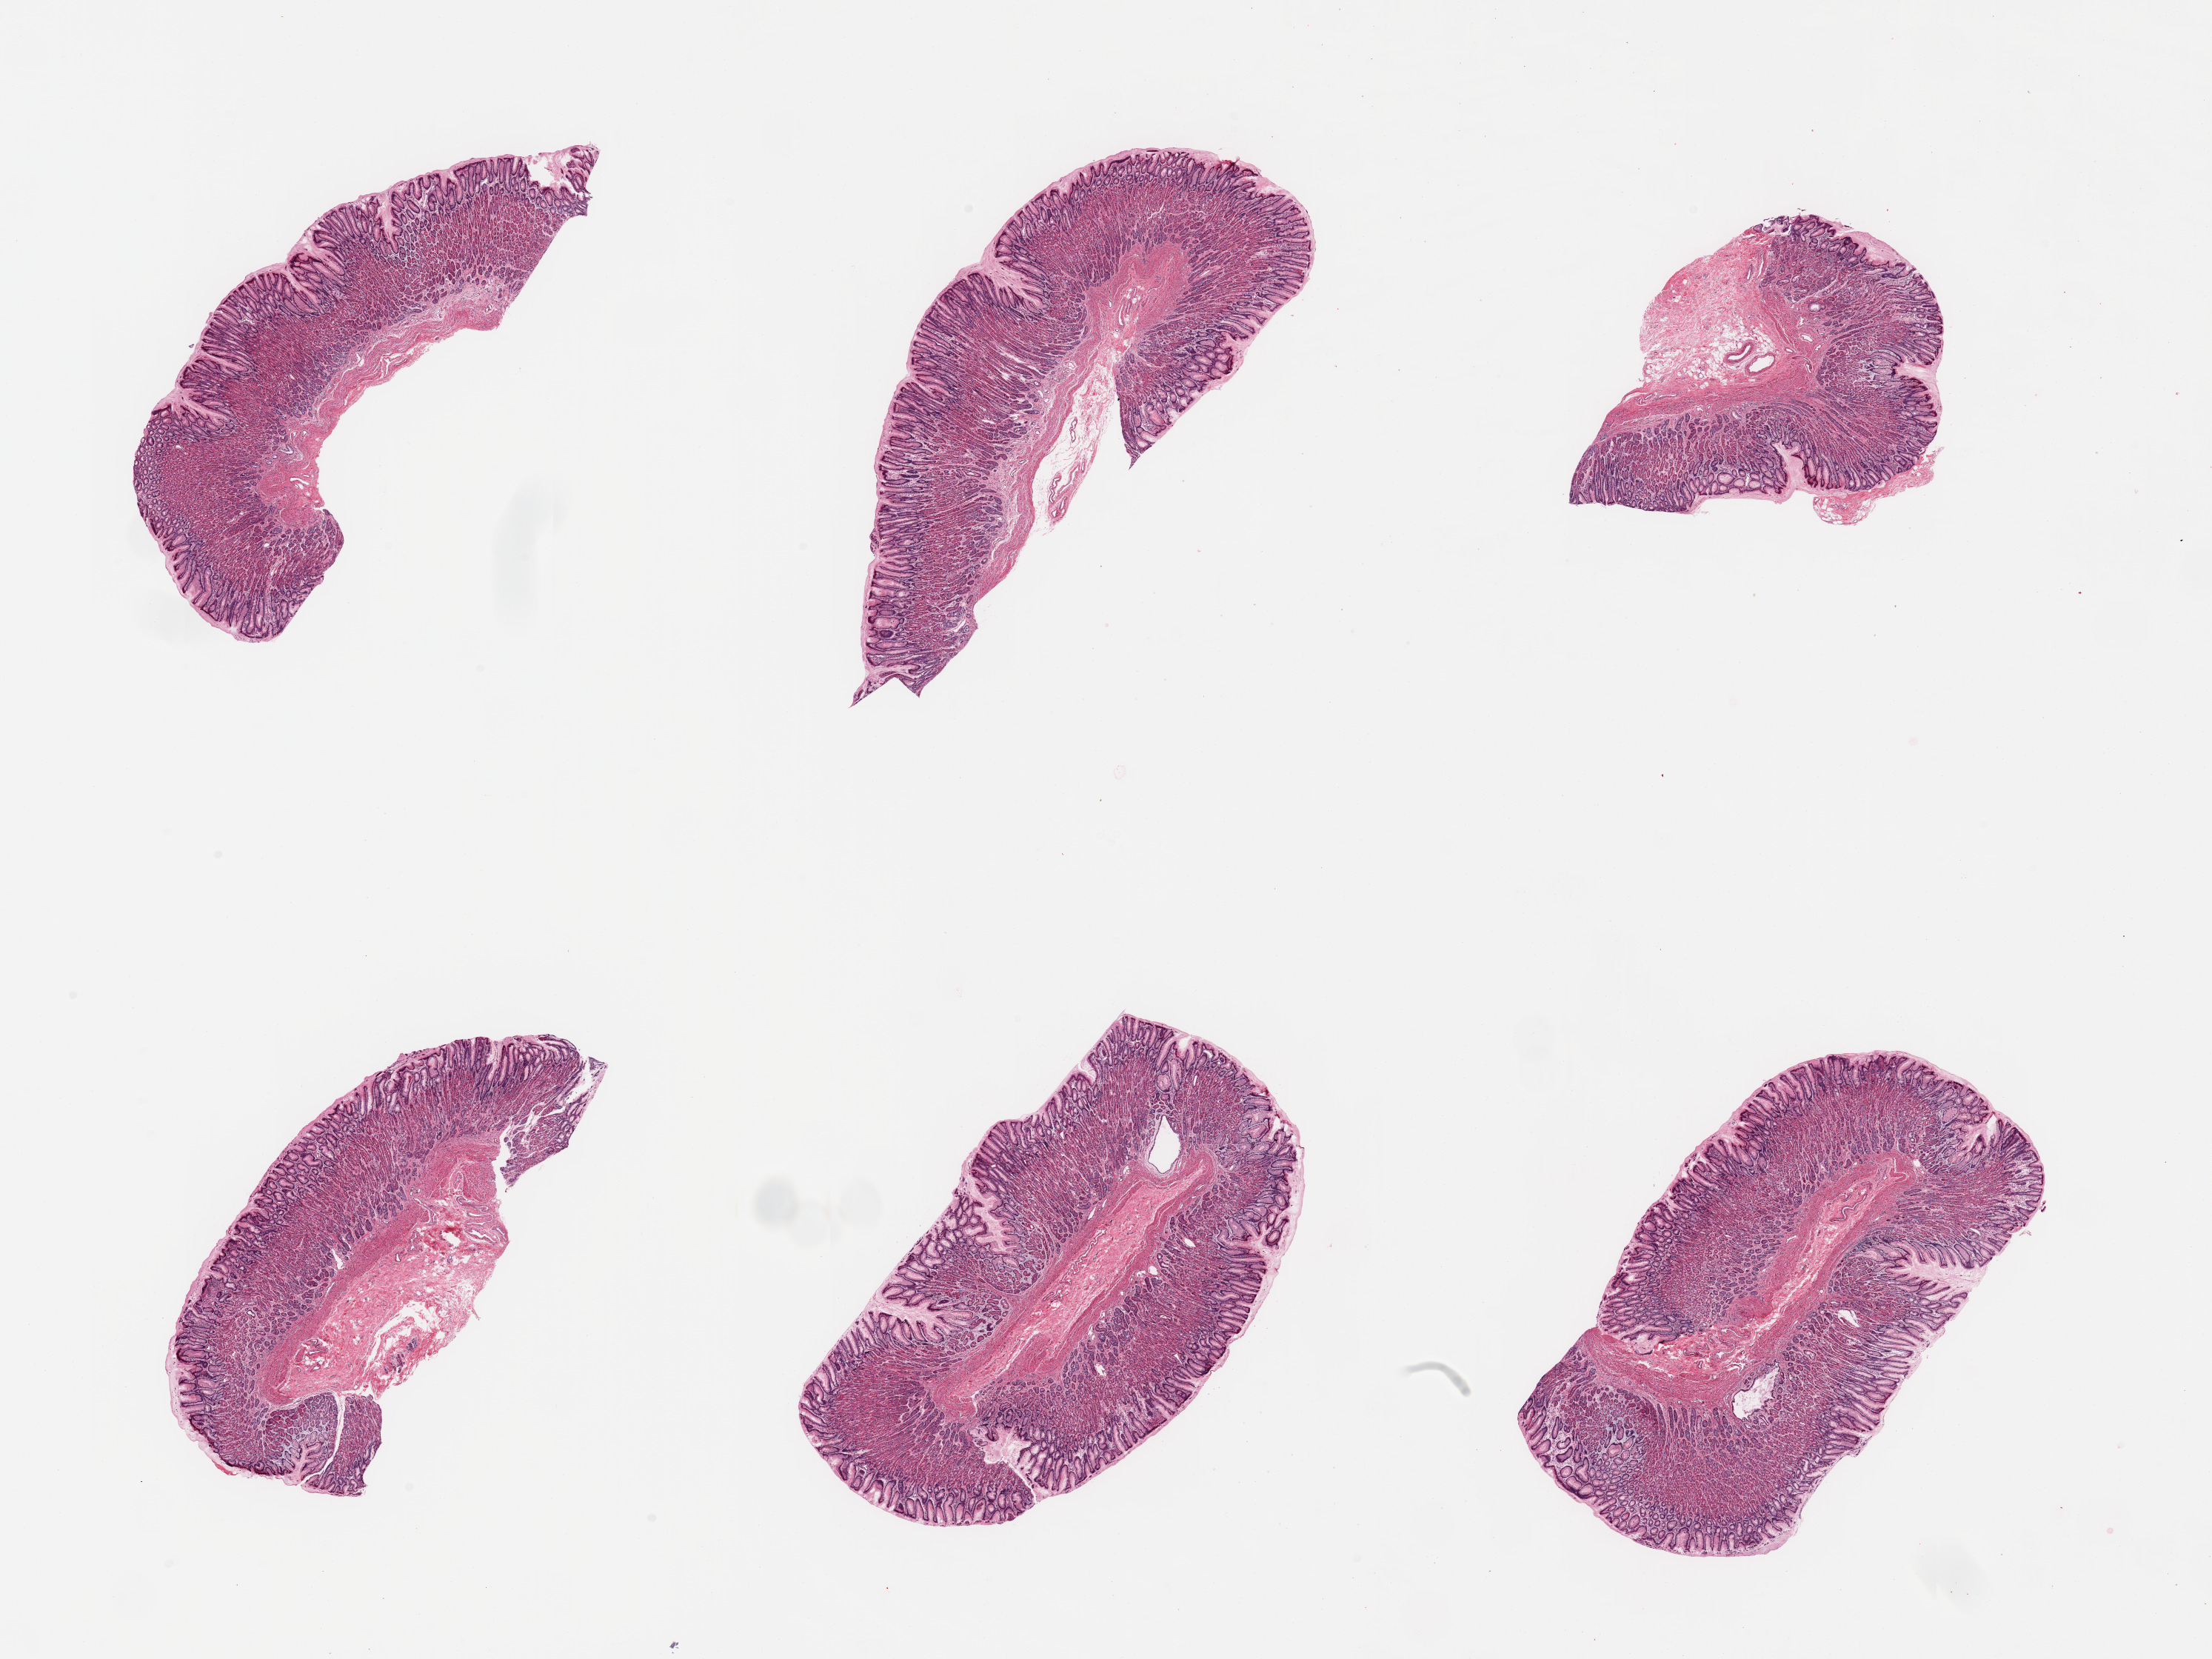
Whole-slide image, hematoxylin and eosin (H&E) stain — low-resolution overview of the scanned area, about 23.6 x 17.7 mm; PAXgene-fixed, paraffin-embedded tissue; sampled site (target tissue): stomach; donor tissue sample.
Pathologist's review note for this sample: 6 pieces, well-preserved mucosa up to ~1.4mm, ~80% of thickness.